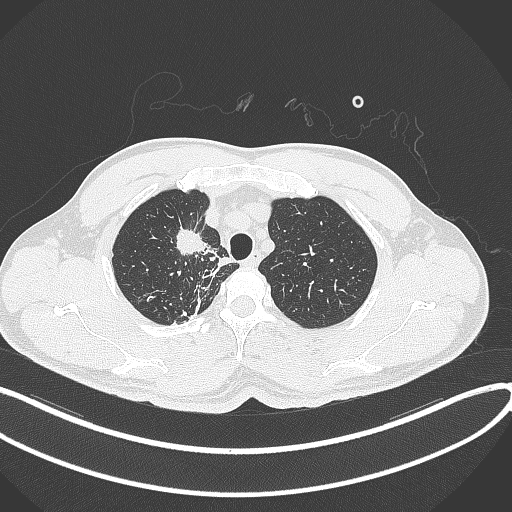
Chest CT, one axial slice. Slice 313 of 391 in the series (ordered by position). 120 kVp. Lung window (W 1500 / L -600 HU). 512 × 512 image matrix, field of view 400 × 400 mm. Male patient, age 48 years. From the clinical record (not read from this slice): clinical TNM (as recorded): T1c N1 M1.
Structures marked on this image (bounding box drawn by a radiologist):
- lung tumour (recorded histology: adenocarcinoma): box from (x=169, y=228) to (x=208, y=260) px